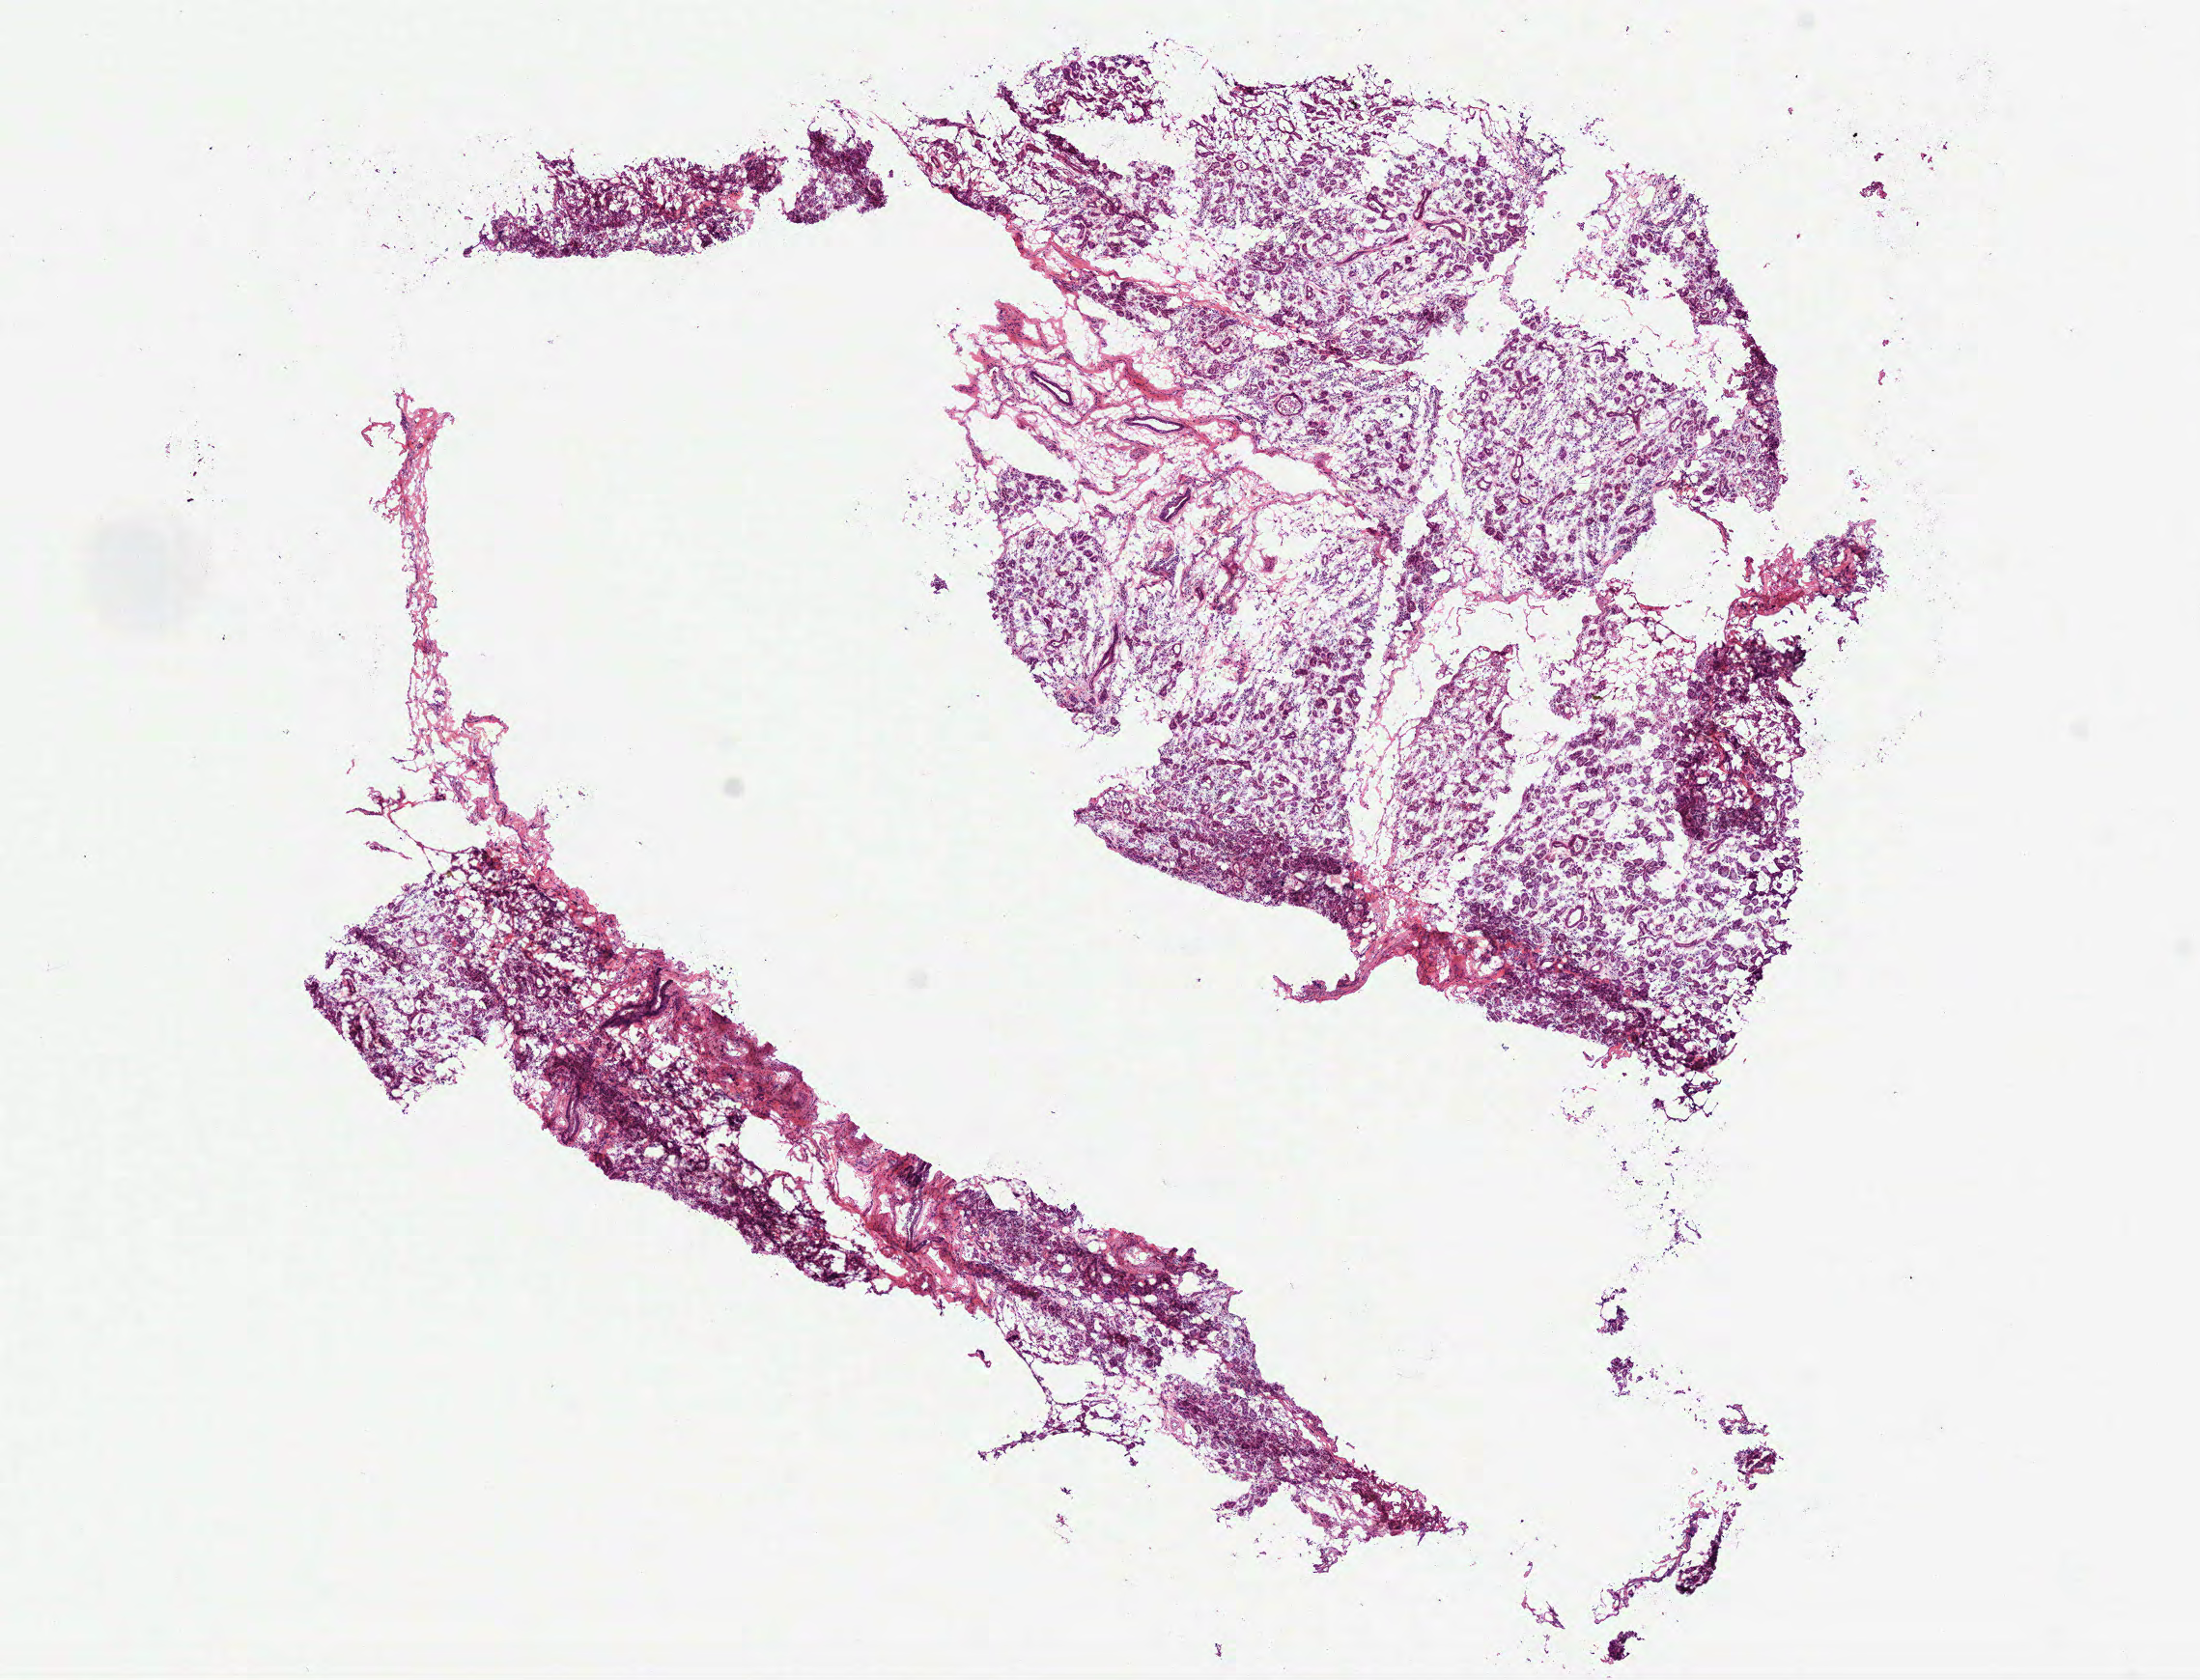
Digitized Hematoxylin and eosin (H&E) stained tissue section (whole slide), a low-resolution overview of the entire scanned area, about 9.2 x 7.0 mm (slide scanned at 40x); frozen section from the top of the tissue portion; sample: solid tissue normal (non-tumour tissue), head and neck. Male patient; age at initial diagnosis 67 years.
* this section: solid tissue normal sample (biorepository sample class)
* patient diagnosis: Squamous cell carcinoma, NOS (floor of mouth, NOS)